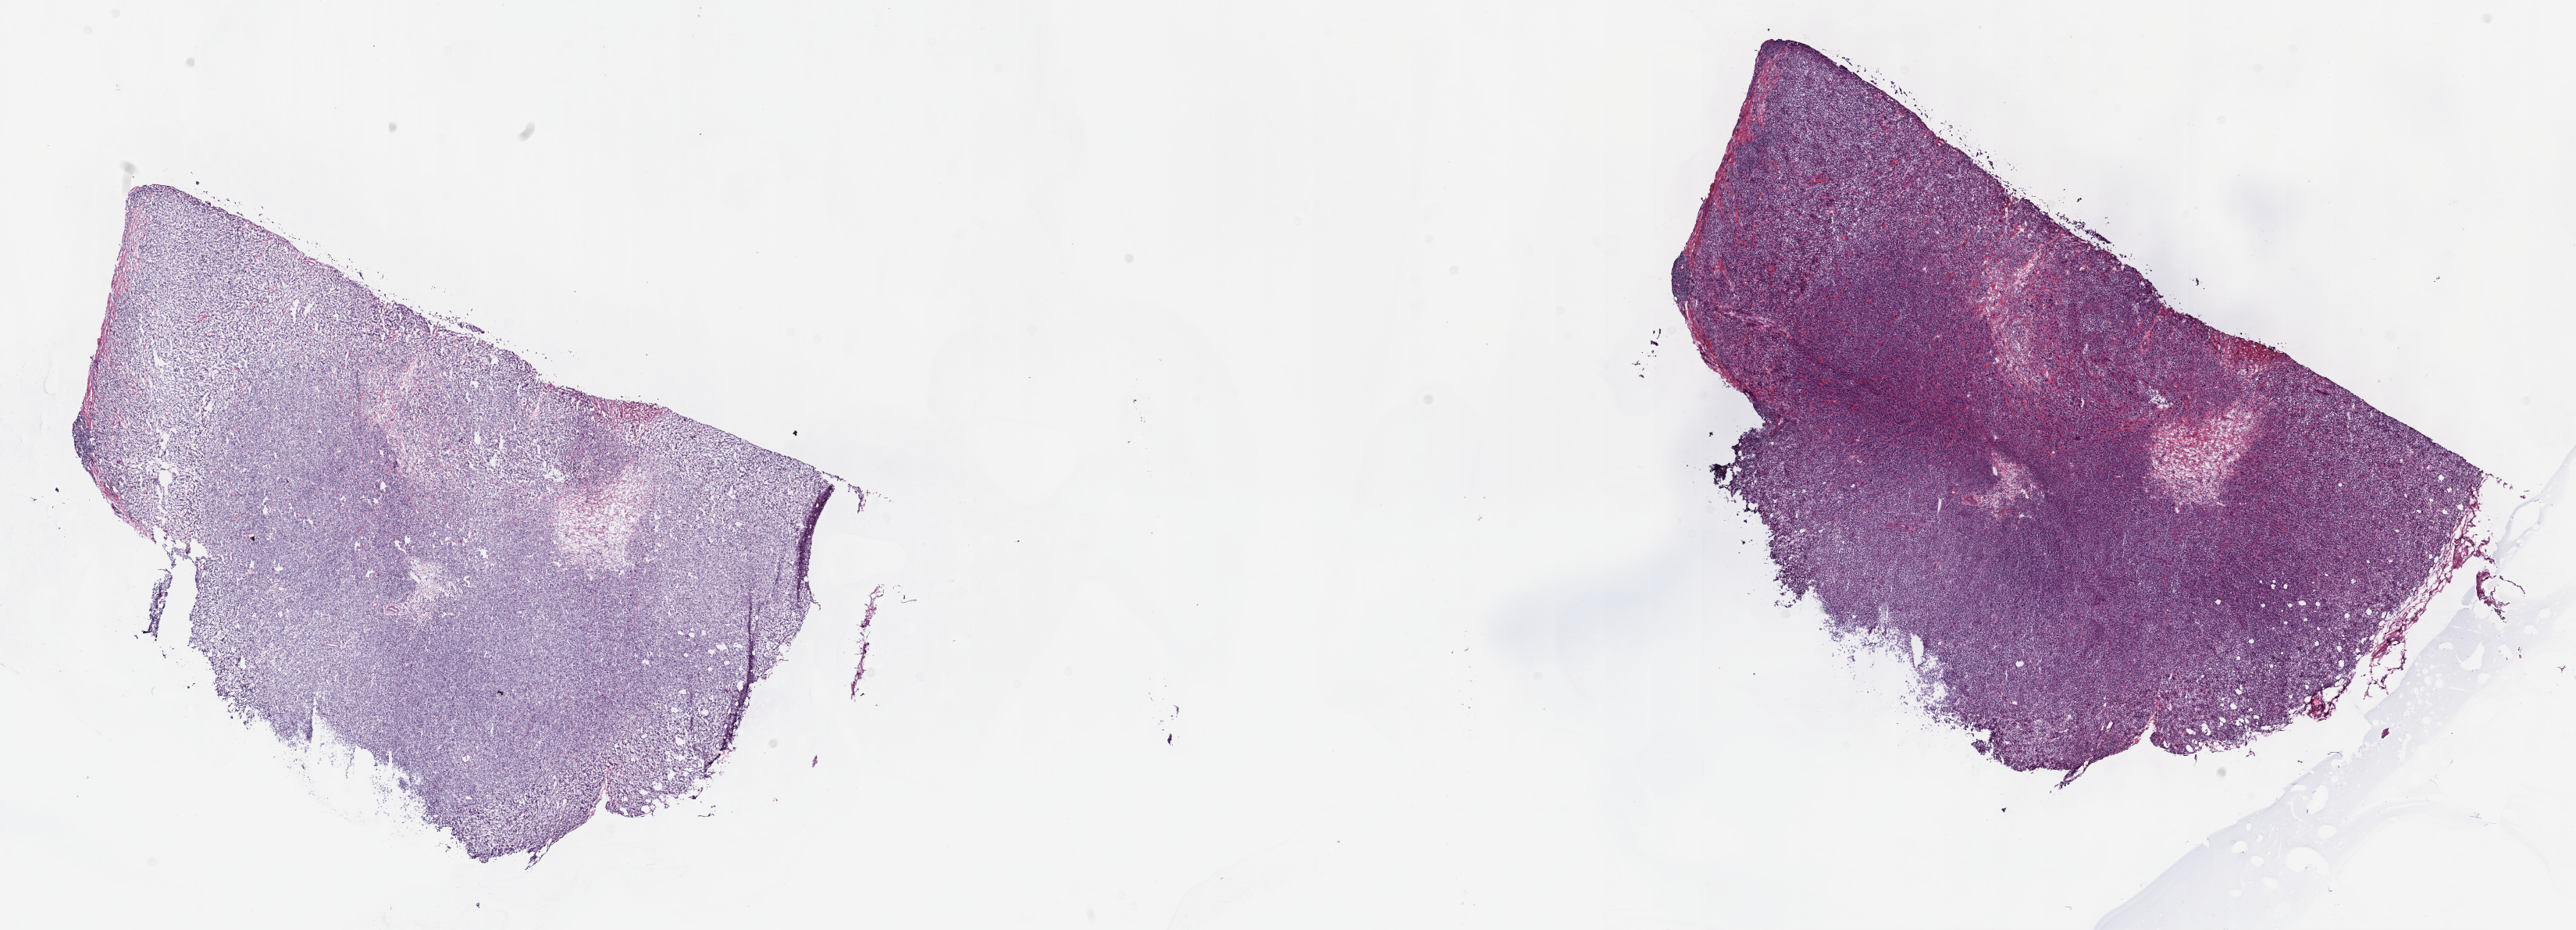
Hematoxylin and eosin (H&E) stained whole-slide image — a low-resolution overview of the entire scanned area, about 26.7 x 9.6 mm (slide scanned at 40x). Frozen section from the top of the tissue portion. Metastatic tumour sample, sampled site: skin of upper limb and shoulder. Female, age 42 years at initial diagnosis. Pathologist review of this section (percent, as recorded): tumour cells 90%, tumour nuclei 80%, normal cells 0%, stromal cells 10%, necrosis 0%. Infiltration values recorded for this section: lymphocyte infiltration 90%, monocyte infiltration 10%, neutrophil infiltration 0%.
This section: metastatic tumour tissue. Patient diagnosis: Malignant melanoma, NOS.